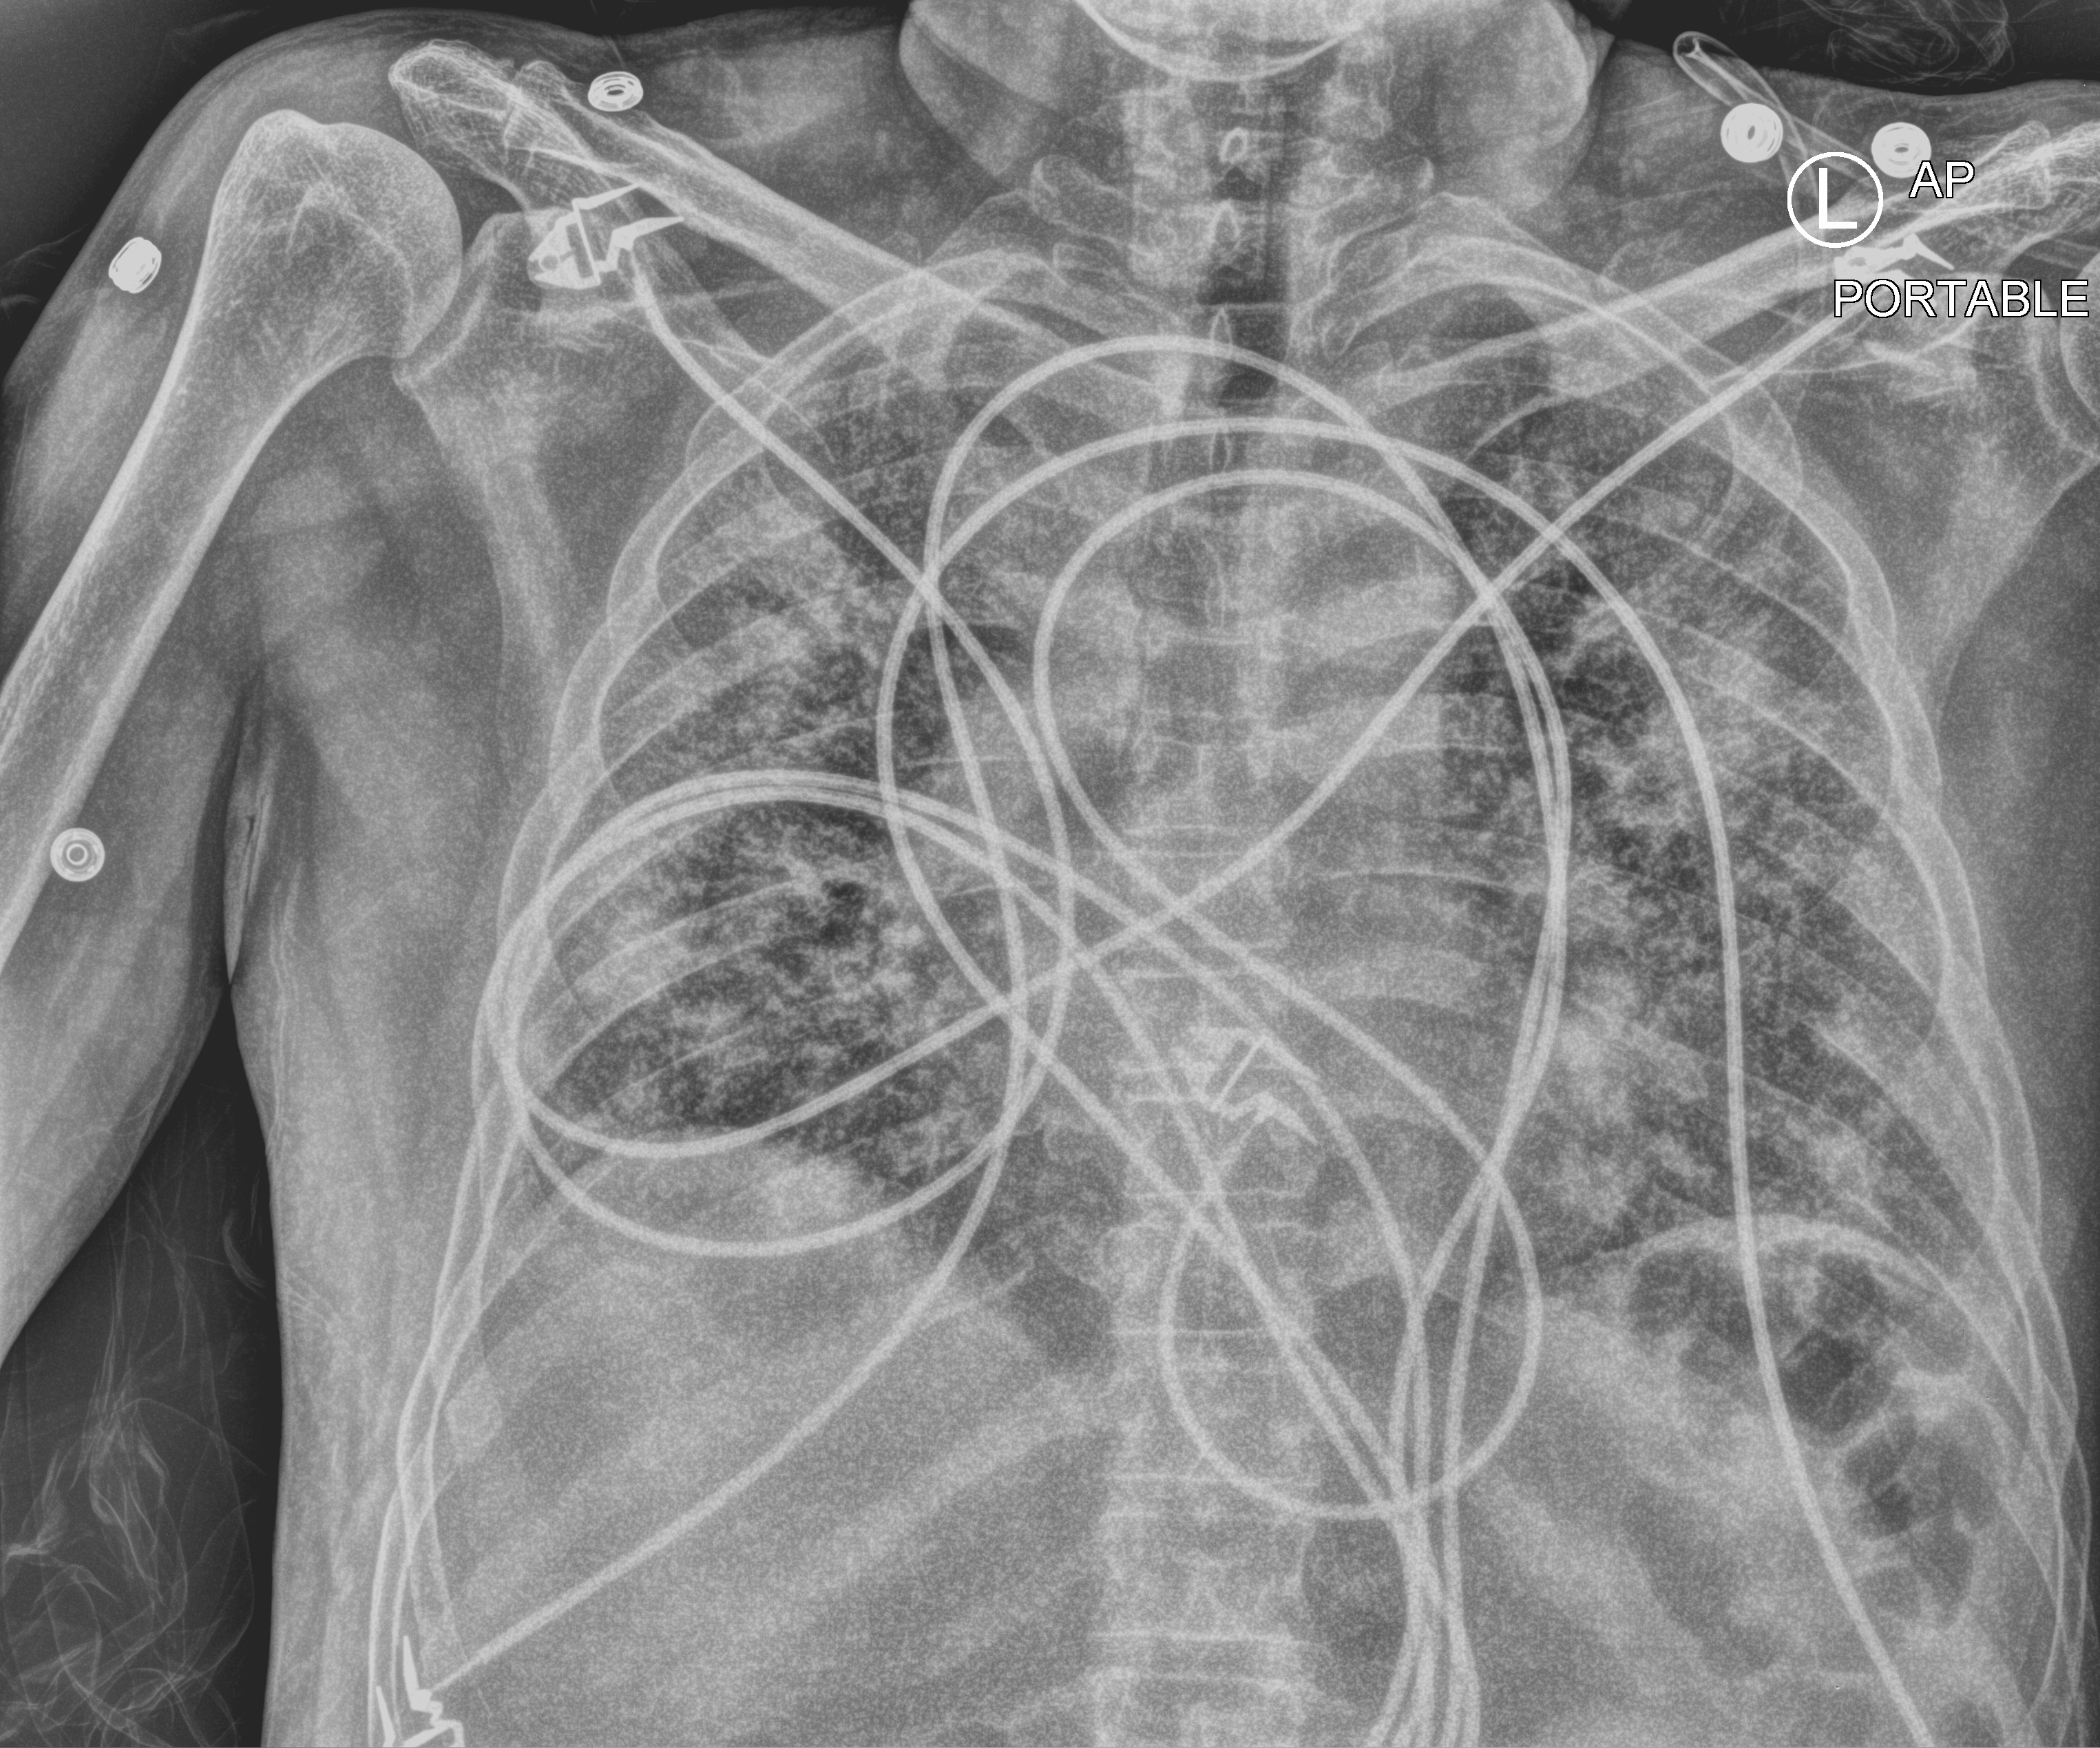
Chest X-ray (portable); anteroposterior (AP) projection. Male patient hospitalised with COVID-19, age 60–74 years.
Admission-level facts for this patient (not findings on this image; timing relative to this image not recorded):
- mechanically ventilated during this hospital stay: yes
- admitted to intensive care during this hospital stay: yes